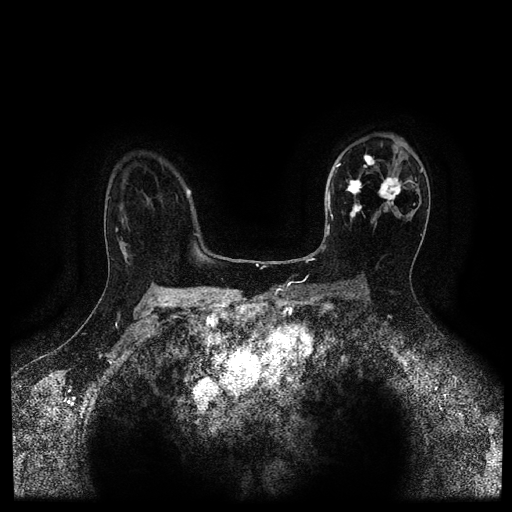
Breast MRI (dynamic contrast-enhanced, multi-phase), one axial slice; position 69 of 116 along the scan axis; dynamic contrast-enhanced series, time point 2 of 5 at this slice position (early post-contrast); 1.5 T; TE 2.7 ms, TR 5.4 ms; 2 mm slice thickness; 512 × 512 image matrix, field of view 340 × 340 mm. Female patient, age 50 years.
Structures marked on this image (semi-automatic segmentation, software-assisted and operator-edited):
- breast lesion (labelled 'tumour' in the annotation; benign lesions carry a separate 'benign' label): bounding box (x1, y1, x2, y2) in pixels: (345, 171, 405, 222)
- breast lesion (labelled 'tumour' in the annotation; benign lesions carry a separate 'benign' label): (363, 154, 377, 168)